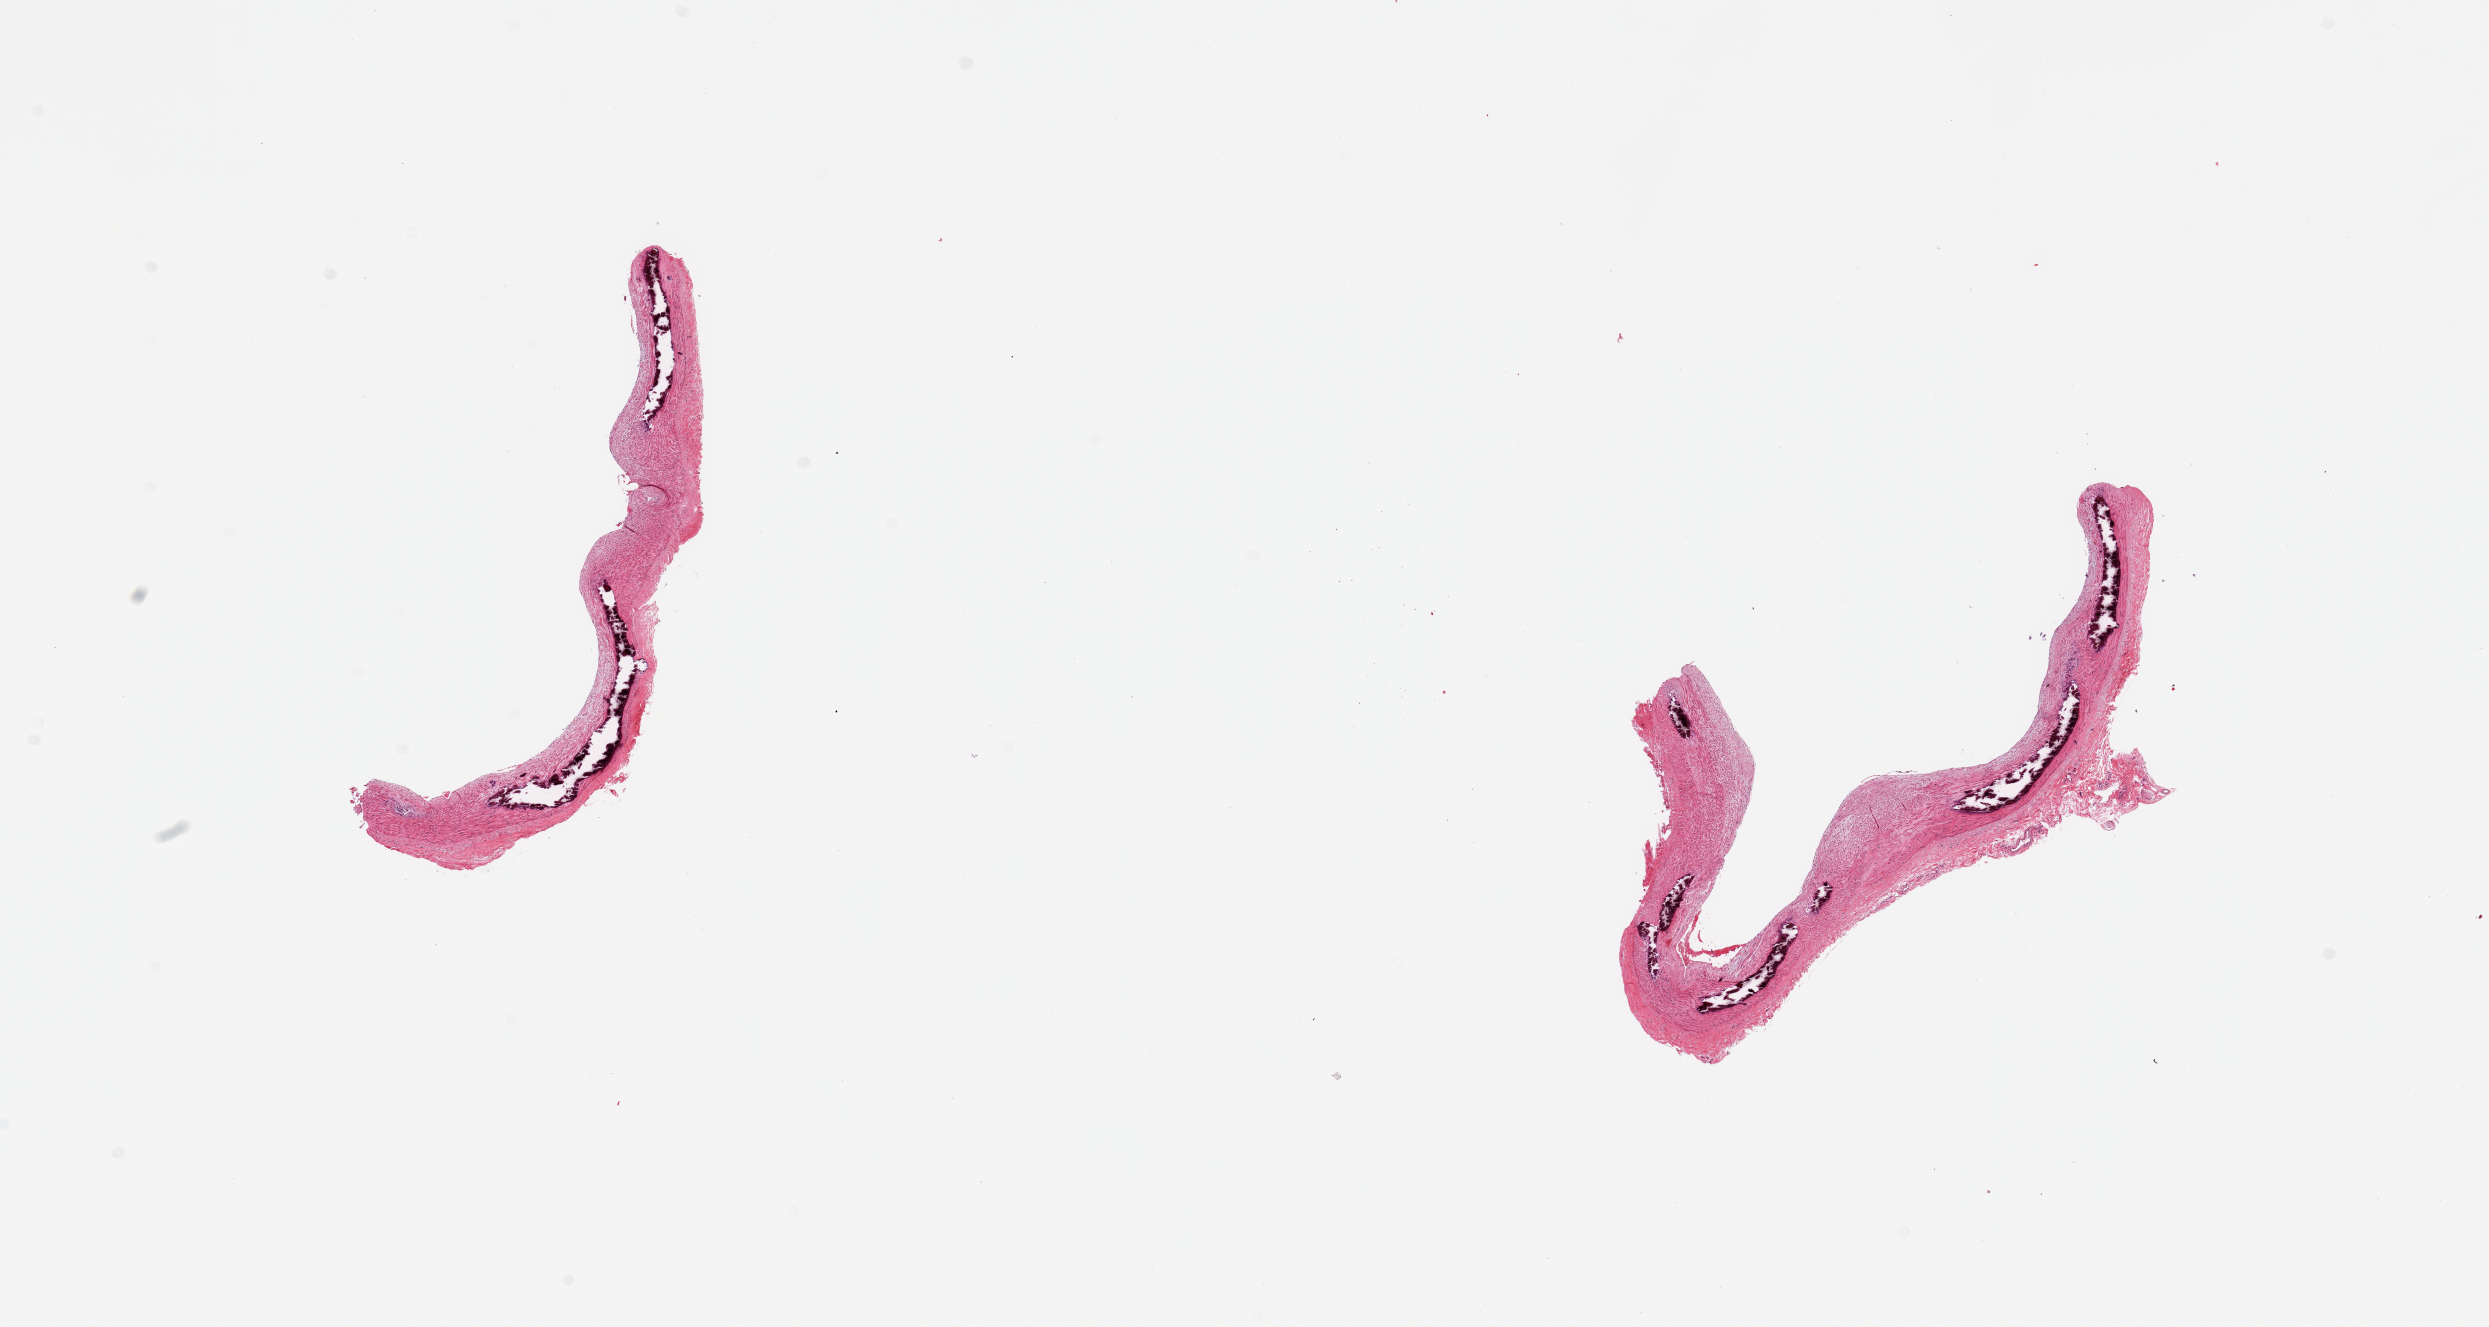
Haematoxylin and eosin whole-slide image, shown as a low-resolution overview of the whole scanned area (about 19.7 x 10.5 mm). PAXgene-fixed, paraffin-embedded tissue. Target tissue: tibial artery. Tissue donor sample. Donor sex: male.
- reviewer comment on this tissue sample: 2 pieces; medial calcific sclerosis